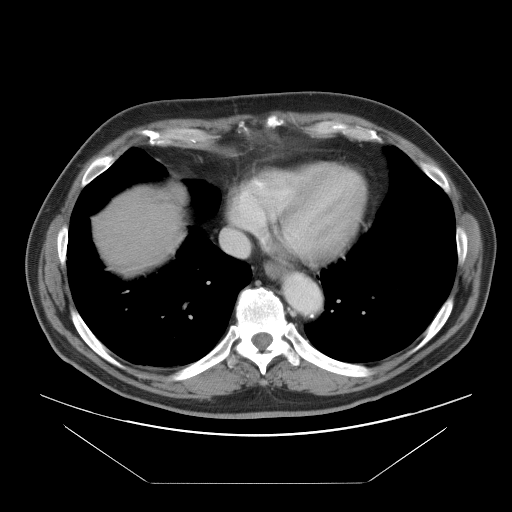
Contrast-enhanced abdominal CT, one axial slice. Slice 88 of 97 in the series (ordered by position). Intravenous contrast given. Soft-tissue window (W 400 / L 40 HU). 512 × 512 image matrix, field of view 442 × 442 mm. Male patient, age 62 years. Case-level facts recorded for this patient, not image findings: diagnosis: colorectal cancer liver metastases, imaged before liver resection; multiple liver metastases: no; largest metastasis: 7 cm; disease in both lobes: yes.
Outlined on this slice (outlined manually by an expert reader):
- hepatic veins: bounding box <221,187,264,258> (left, top, right, bottom; pixels)
- liver: <99,191,180,268>
- planned liver remnant (the part of the liver to remain after resection): <100,193,181,267>